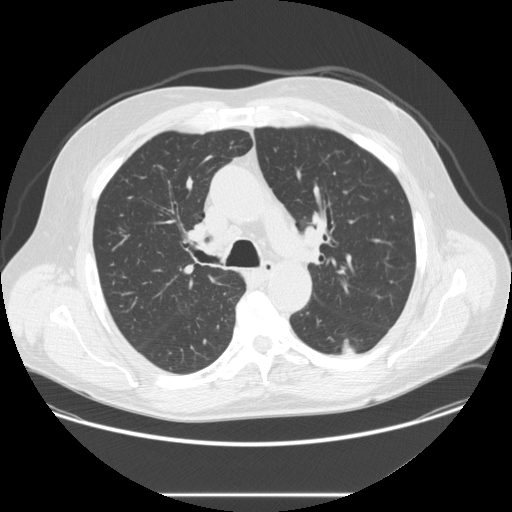
Low-dose screening chest CT, one axial slice; slice 174 of 262 in the series (ordered by position); reconstruction kernel STANDARD; 120 kVp; lung window (W 1500 / L -600 HU); 2.5 mm slice thickness; 512 × 512 image matrix, field of view 420 × 420 mm.
Outlined on this slice (manually delineated by an expert):
- lesion 1 (tumor, lower lobe of left lung): bounding box [x1, y1, x2, y2] px = [342, 342, 356, 355]